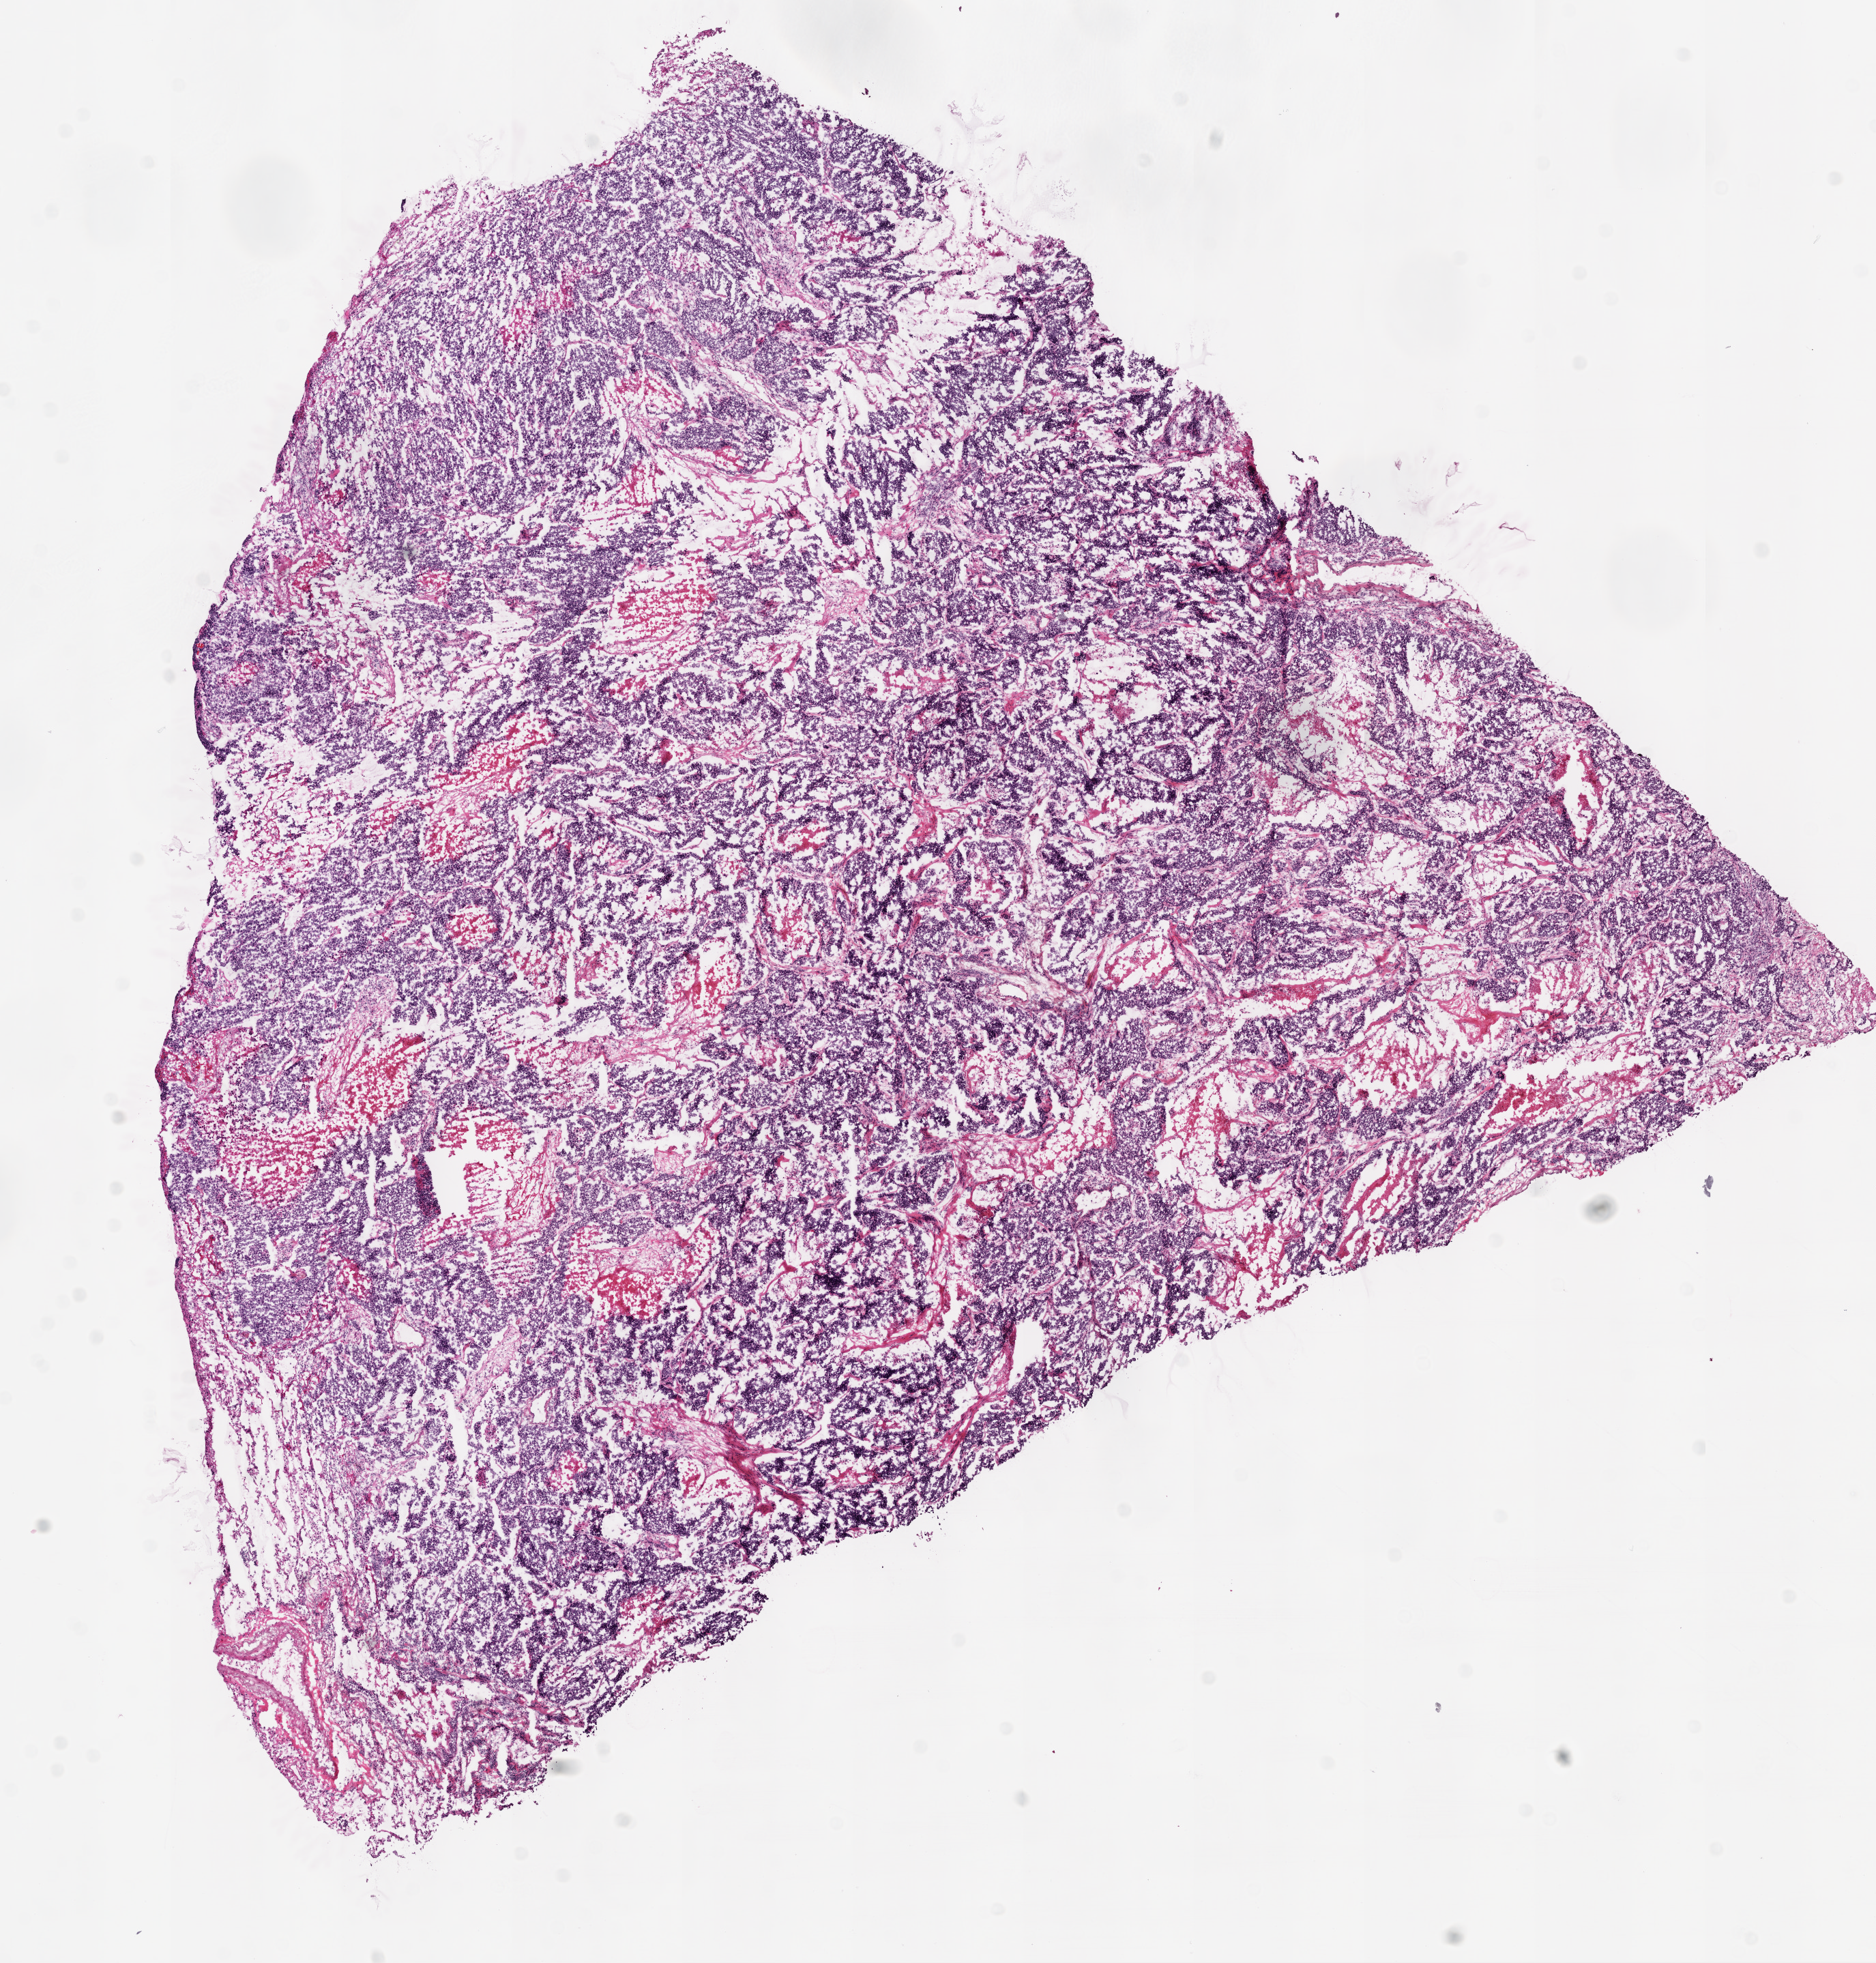
Digitized H&E tissue section (whole slide), a low-resolution overview of the entire scanned area, about 11.0 x 11.5 mm (slide scanned at 20x), frozen section, lung, primary tumour sample. Male, age 68 years at initial diagnosis. Slide review estimates, as recorded: tumour cells 75%, tumour nuclei 85%, normal cells 5%, stromal cells 5%, necrosis 15%.
TNM: T2a N0 M0. Laterality: right. Histologic diagnosis: Squamous cell carcinoma, NOS (lower lobe, lung). AJCC pathologic stage: IB.